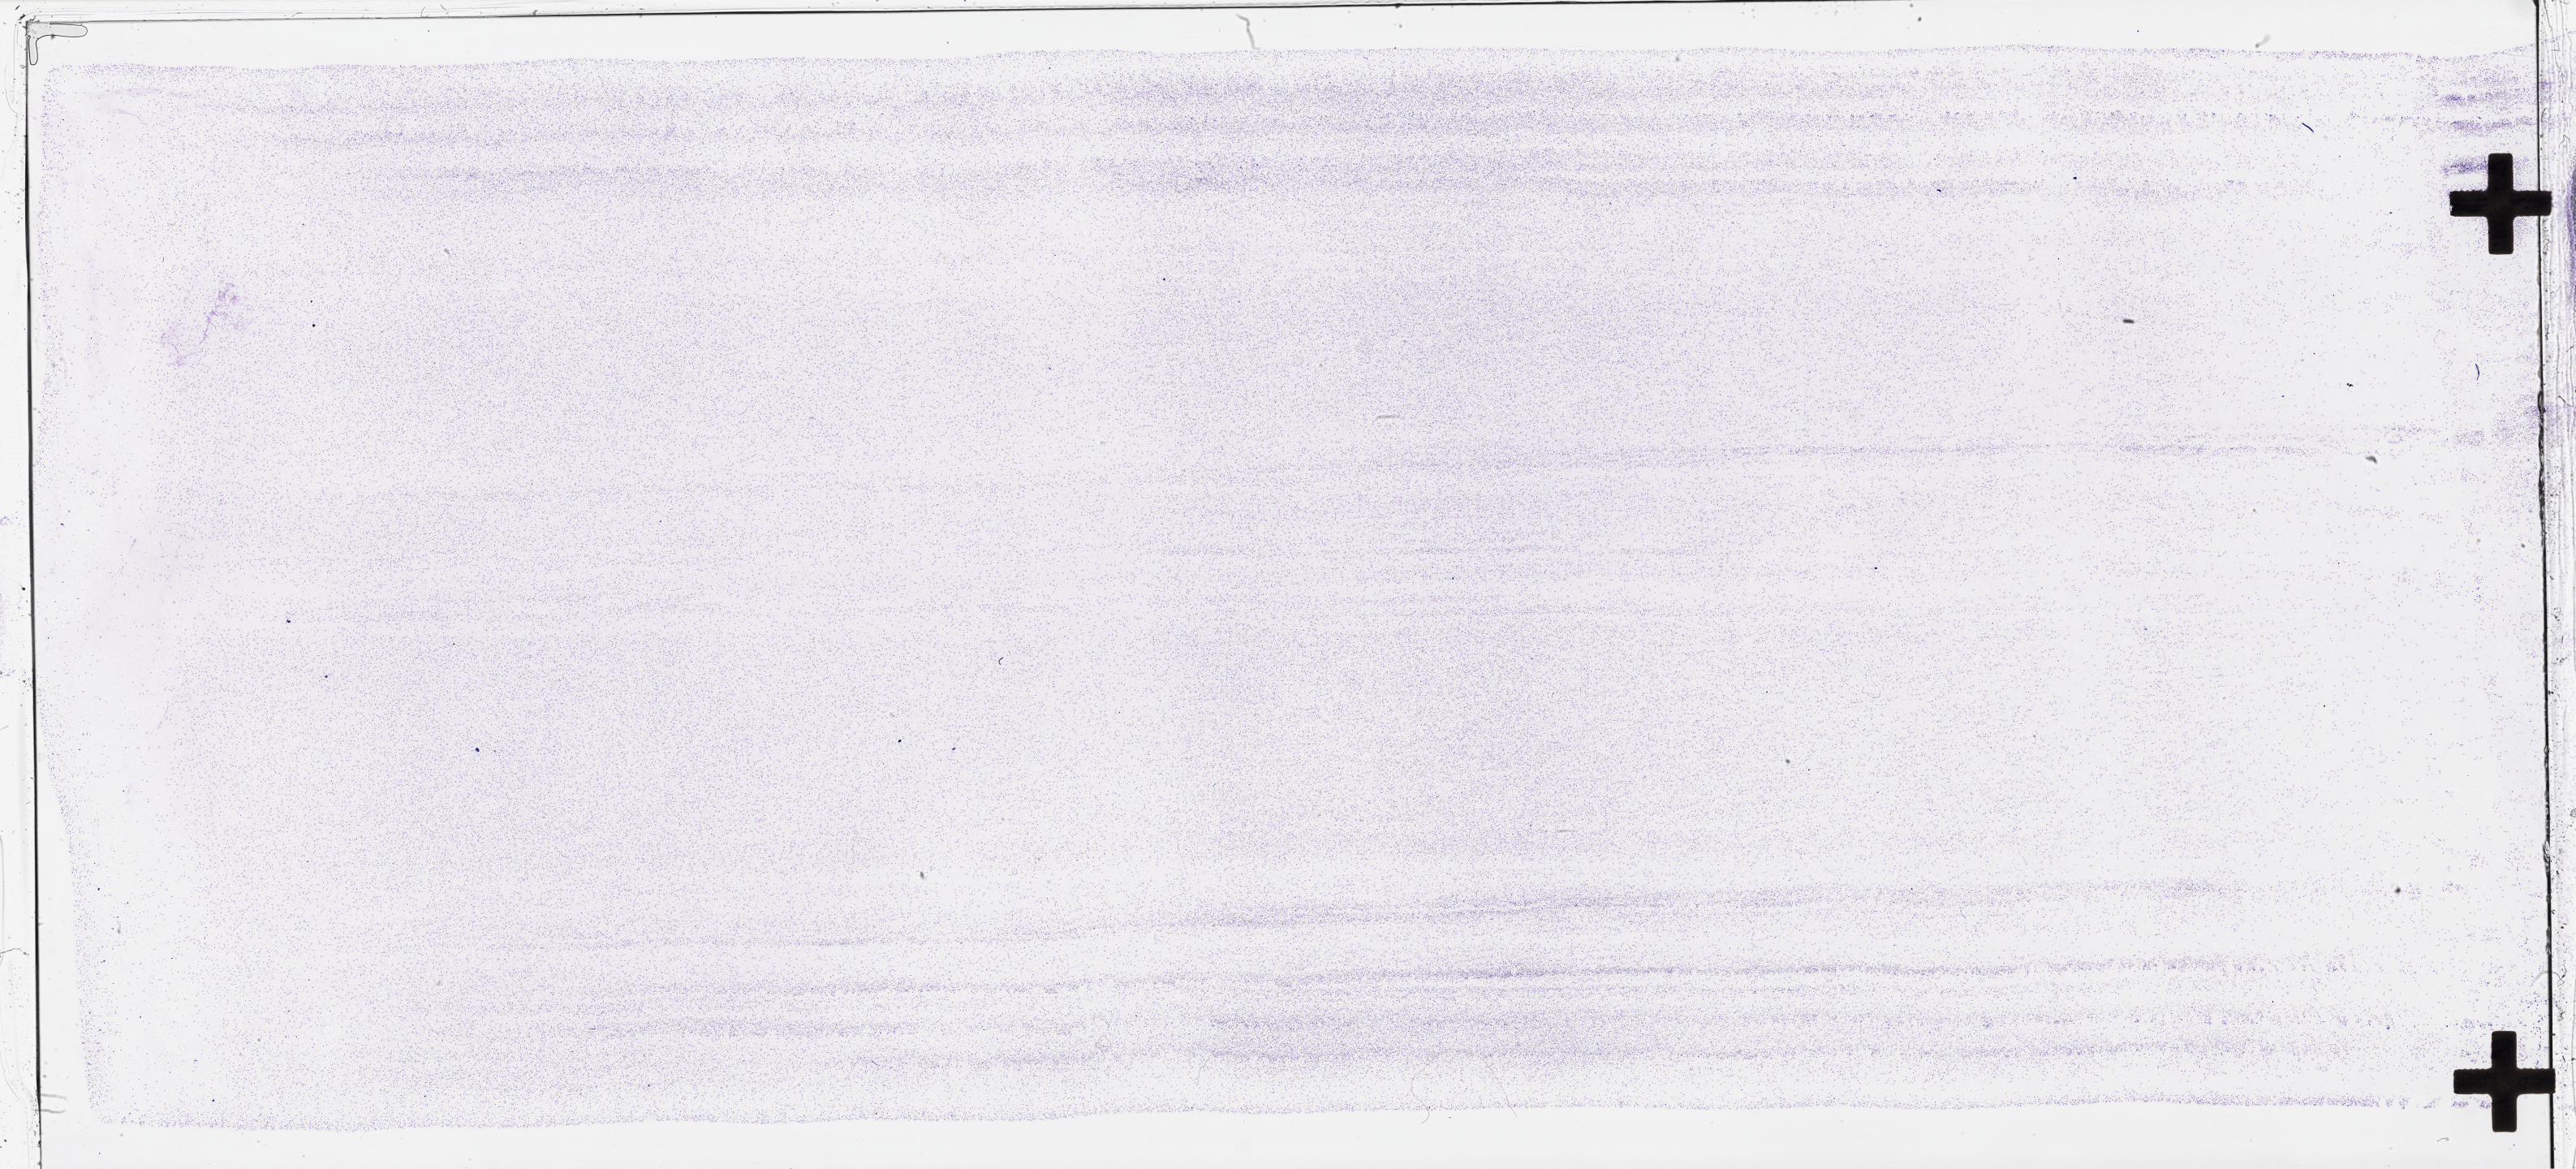
Digitized H&E-stained tissue section (whole slide) — whole scanned area (about 51.3 x 23.3 mm, from a 40x scan) shown as a low-resolution overview, peripheral blood (leukaemic) sample. Male, 18 y/o.
Diagnosis: Acute Myeloid Leukemia. FAB classification: M1.